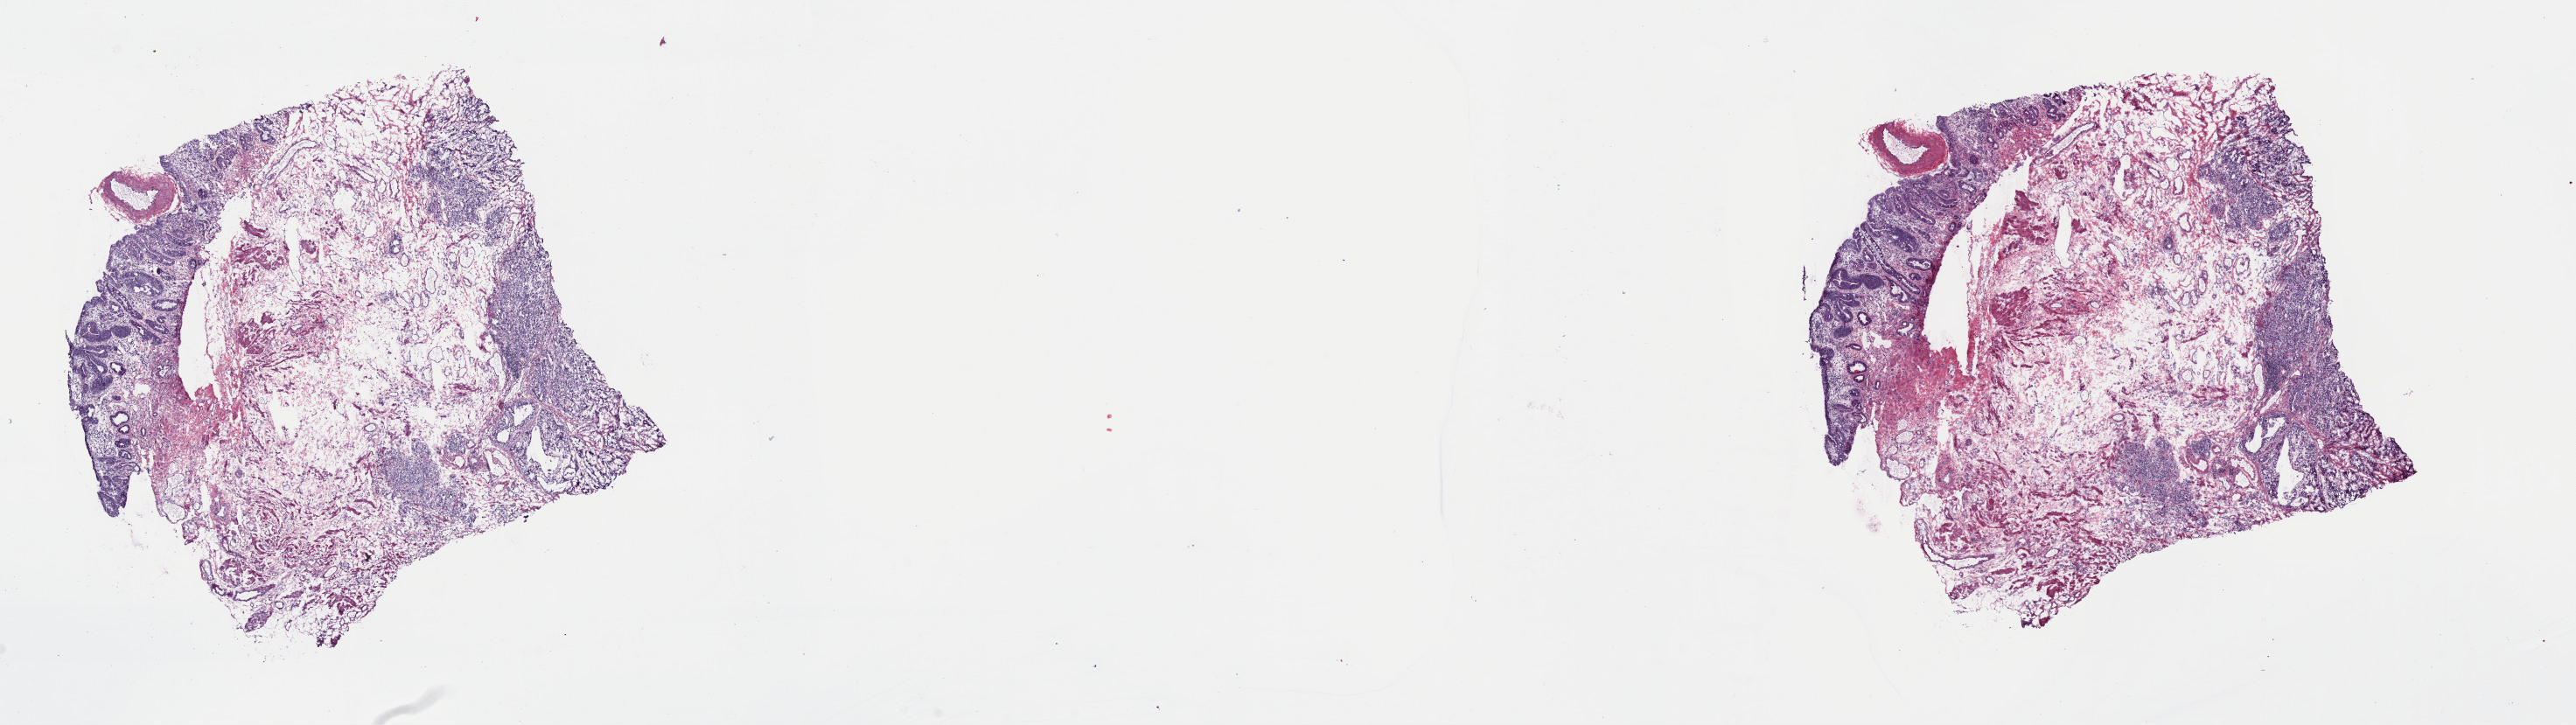
H&E whole-slide image, shown as a low-resolution overview of the whole scanned area (about 23.3 x 6.5 mm, acquisition: 40x scan). Frozen section from the top of the tissue portion. Sample: primary tumour, esophagus. Male patient; age at initial diagnosis 63 years. Histologic grade: G3 (poorly differentiated). Pathologist review of this section (percent, as recorded): tumour cells 60%, tumour nuclei 60%, normal cells 10%, stromal cells 30%, necrosis 0%. Infiltration values recorded for this section: lymphocyte infiltration 10%, monocyte infiltration 0%, neutrophil infiltration 0%.
Diagnosis: Adenocarcinoma, NOS. Lymph nodes positive (case pathology): 1 of 18 examined. AJCC pathologic stage: IIB (7th edition).